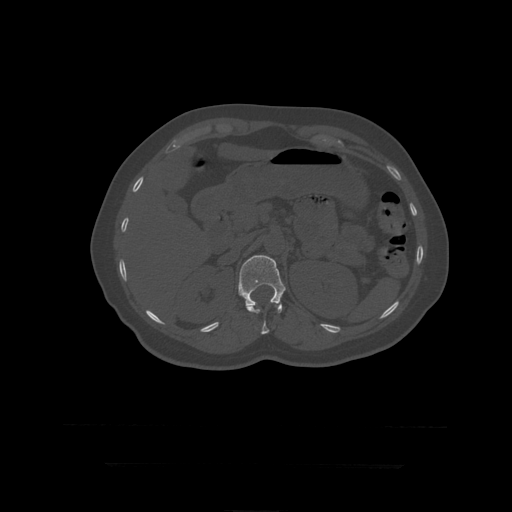
CT including the spine, one axial slice; slice 183 of 399 in the series (ordered by position); bone window (W 1800 / L 400 HU); 1.25 mm slice thickness; 512 × 512 image matrix, field of view 450 × 450 mm. Patient age 41 years. From the clinical record (not read from this slice): primary cancer: breast.
Outlined on this slice (semi-automatically segmented with operator editing):
- L1 vertebra: box from (x=238, y=255) to (x=286, y=314) px
- T12 vertebra: (x=246, y=304)–(x=282, y=335)